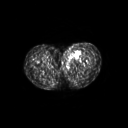
FDG PET of an extremity soft-tissue mass (from a PET/CT study), one axial slice; position 44 of 267 along the scan axis; 128 × 128 image matrix, field of view 600 × 600 mm. Patient: female, 24 years. From the clinical record (not read from this slice): histological type: leiomyosarcoma; grade: high; site of the primary tumour: groin.
Outlined on this slice (expert contour drawn on MRI and transferred to this co-registered scan by the dataset authors):
- gross tumour volume including surrounding oedema: bounding box [x1, y1, x2, y2] px = [61, 47, 80, 64]
- gross tumour volume (mass): [72, 51, 79, 56]